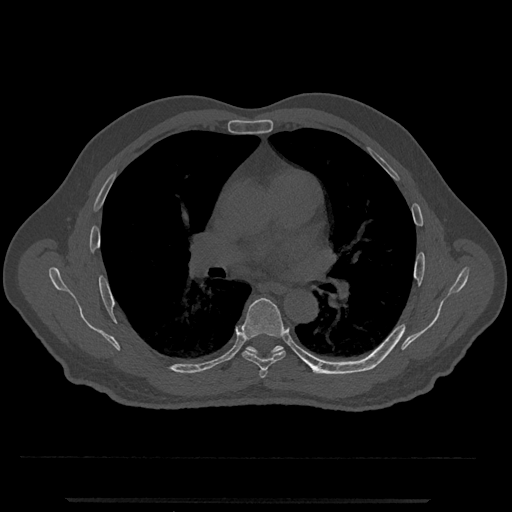
CT including the spine, one axial slice; slice 725 of 797 in the series (ordered by position); reconstruction kernel Br40s/3; 120 kVp; bone window (W 1800 / L 400 HU); 0.5 mm slice thickness; 512 × 512 image matrix, field of view 419 × 419 mm. Patient: male, 63 years. Case-level facts recorded for this patient, not image findings: primary cancer: prostate.
Annotated regions visible in this slice (semi-automatically segmented with operator editing):
- T5 vertebra: box from (x=259, y=369) to (x=268, y=378) px
- T6 vertebra: (x=240, y=298)–(x=286, y=371)
- T7 vertebra: (x=246, y=345)–(x=329, y=375)